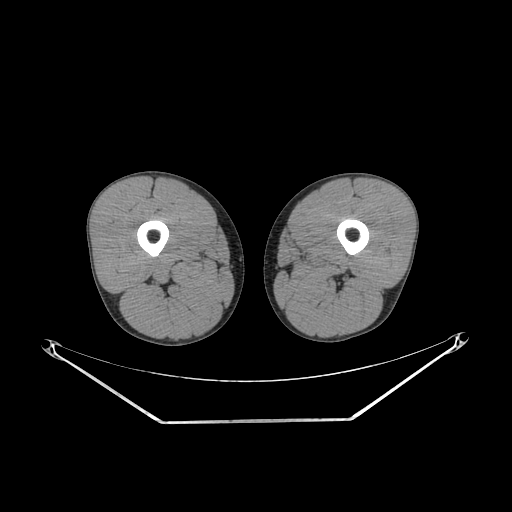
CT of an extremity soft-tissue mass (from a PET/CT study), one axial slice; position 215 of 267 along the scan axis; soft-tissue window (W 400 / L 40 HU); 512 × 512 image matrix, field of view 500 × 500 mm. Male patient. From the clinical record (not read from this slice): histological type: extraskeletal osteosarcoma; grade: high; site of the primary tumour: left adductur.
Annotated regions visible in this slice (expert contour drawn on MRI and transferred to this co-registered scan by the dataset authors):
- gross tumour volume (mass): box from (x=308, y=253) to (x=350, y=271) px